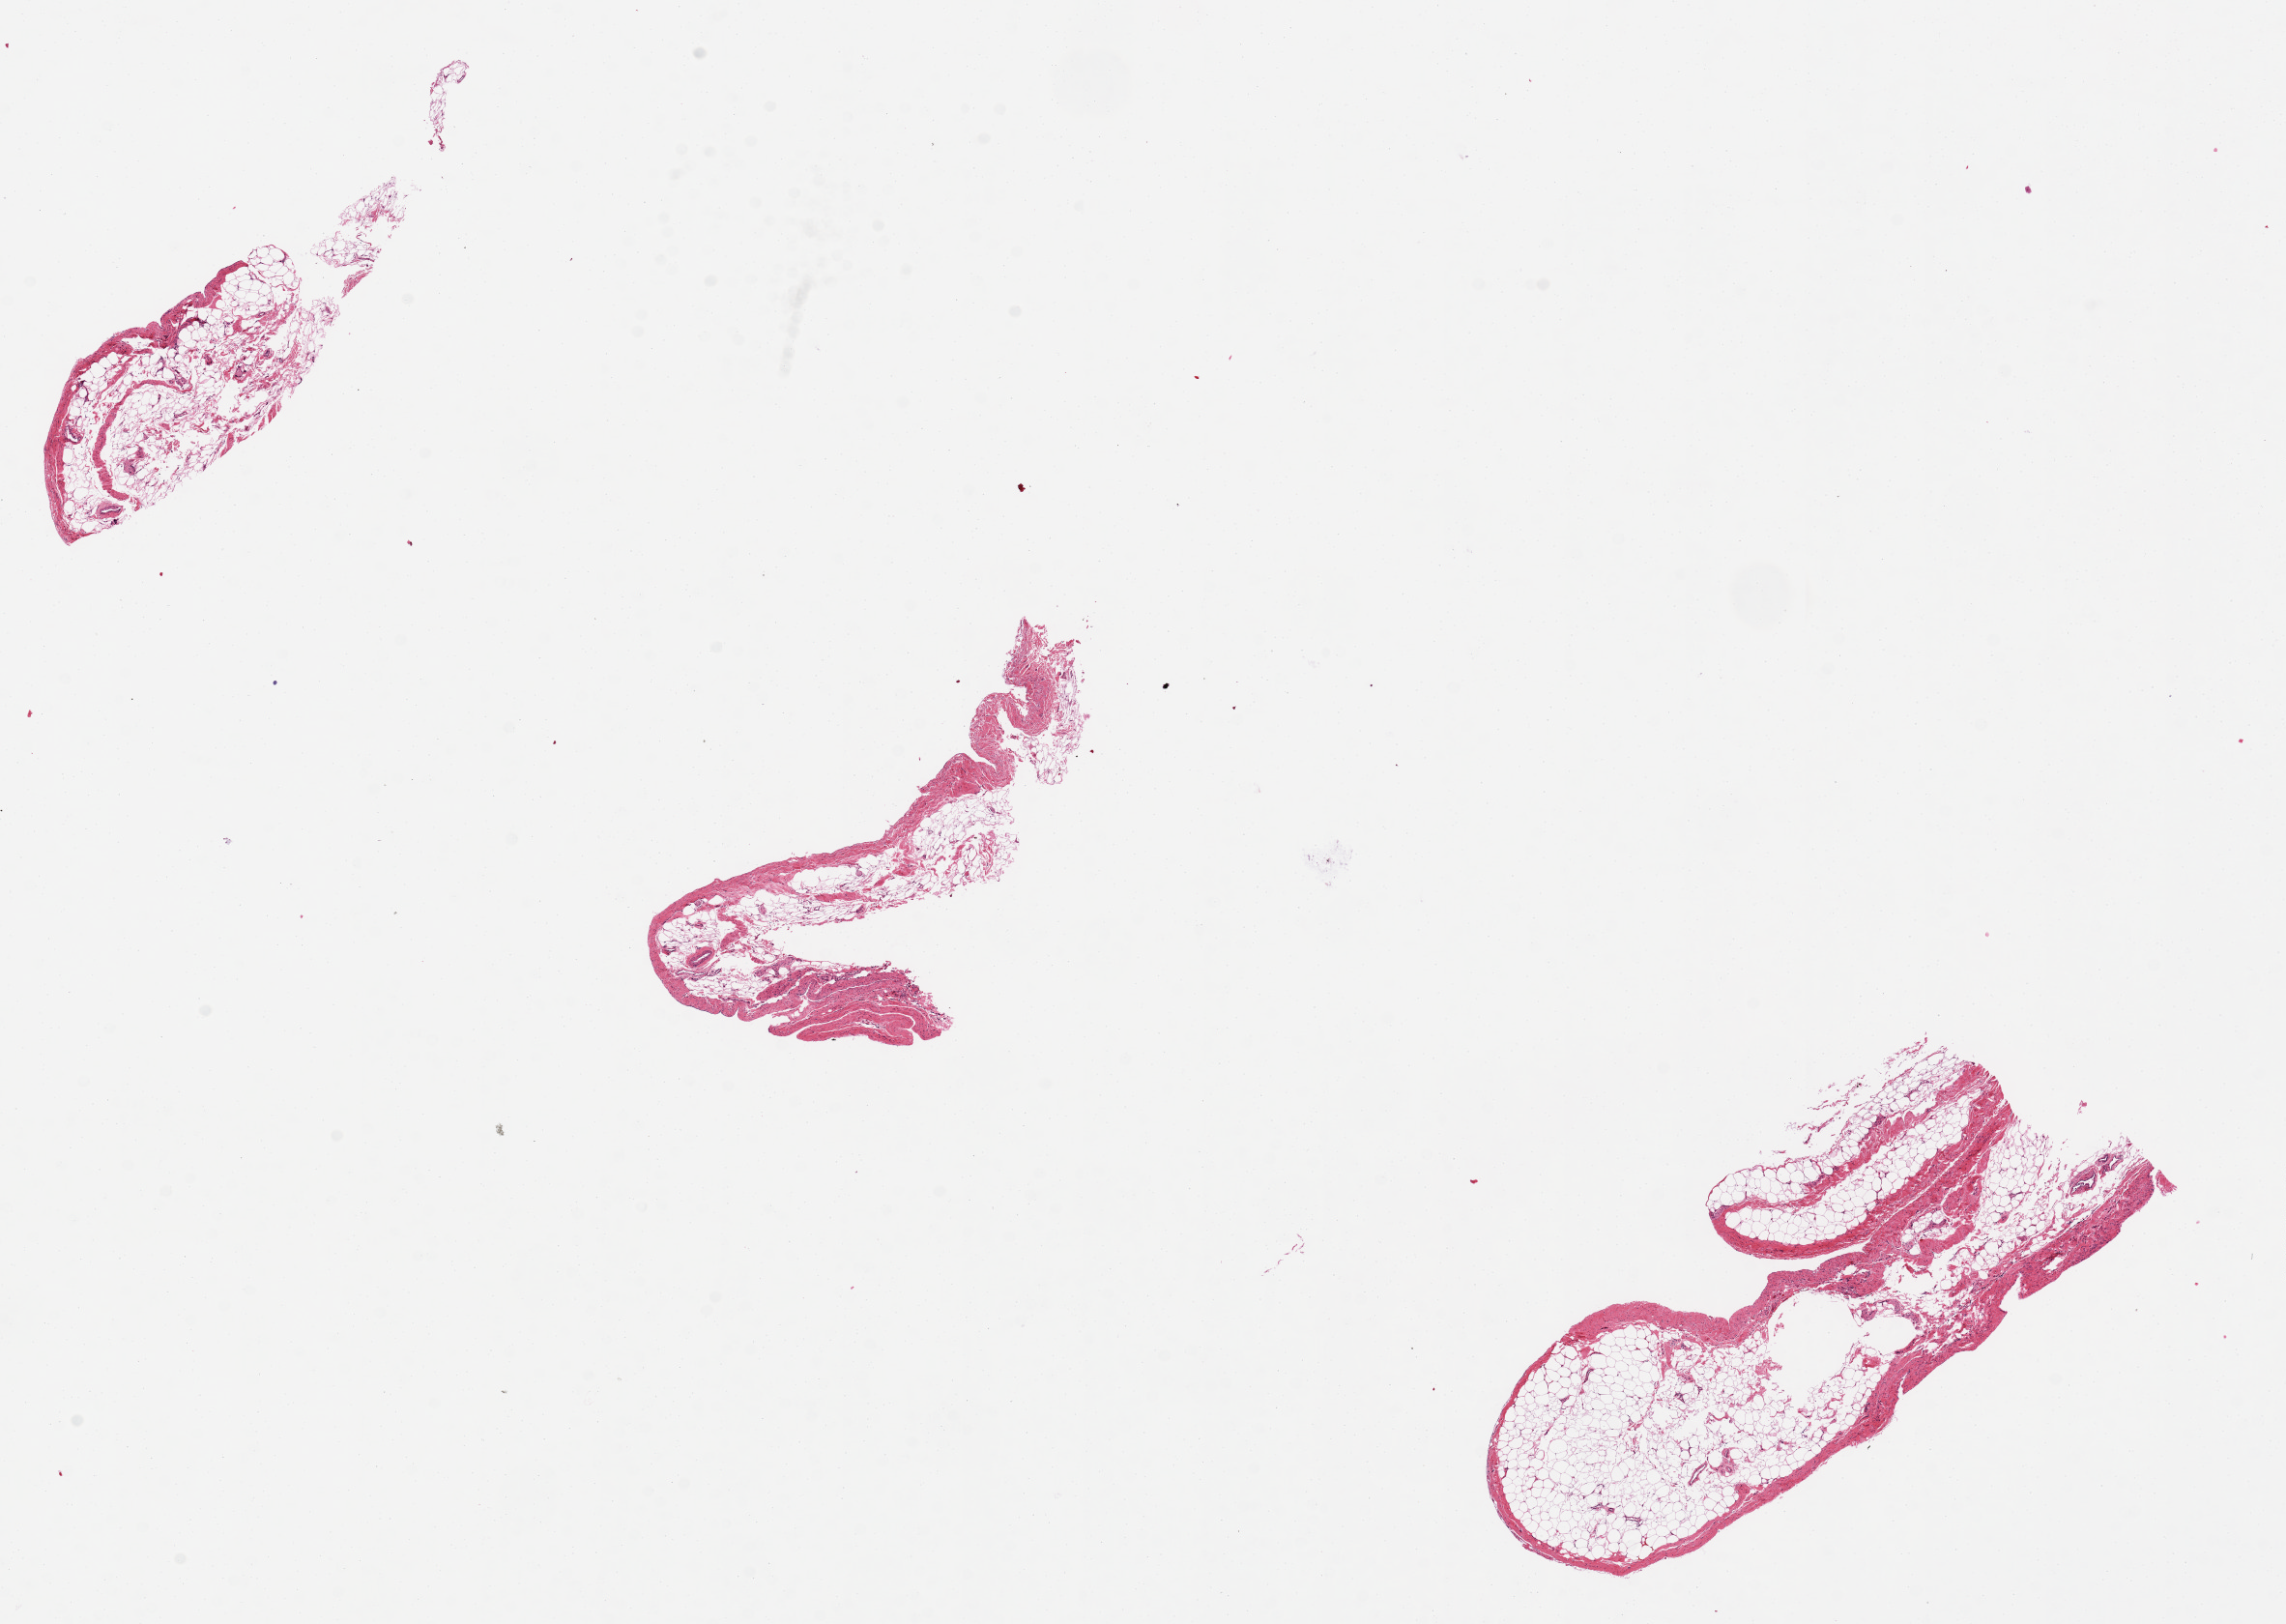
Whole-slide image, haematoxylin and eosin stain, a low-resolution overview of the entire scanned area, about 18.7 x 13.3 mm, PAXgene-fixed paraffin-embedded (PFPE) section, sampled site (target tissue): urinary bladder, tissue donor sample. Donor sex: male.
Reviewer comment on this tissue sample: Fatty fibromuscular and neural tissue, no sign of surface epithelium; 3 pieces, origin unclear; 6x2mm.